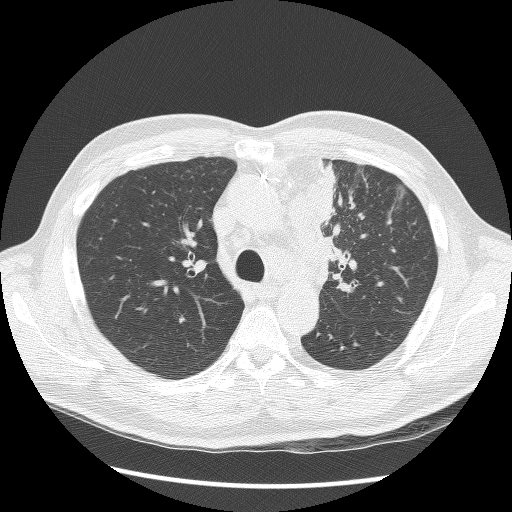
Chest CT (low-dose screening protocol), one axial image; second screening round (one year after baseline); lung window (W 1500 / L -600 HU); 2.5 mm slice thickness; 512 × 512 image matrix, field of view 360 × 360 mm. Male participant, aged 64 years at enrolment. Former smoker at enrolment.
Expert-annotated lung lesion, bounding box [x1, y1, x2, y2] px = [298, 167, 370, 290]. Screening reader's record for this exam: no non-calcified nodule ≥4 mm recorded. Official screen result: positive, other.